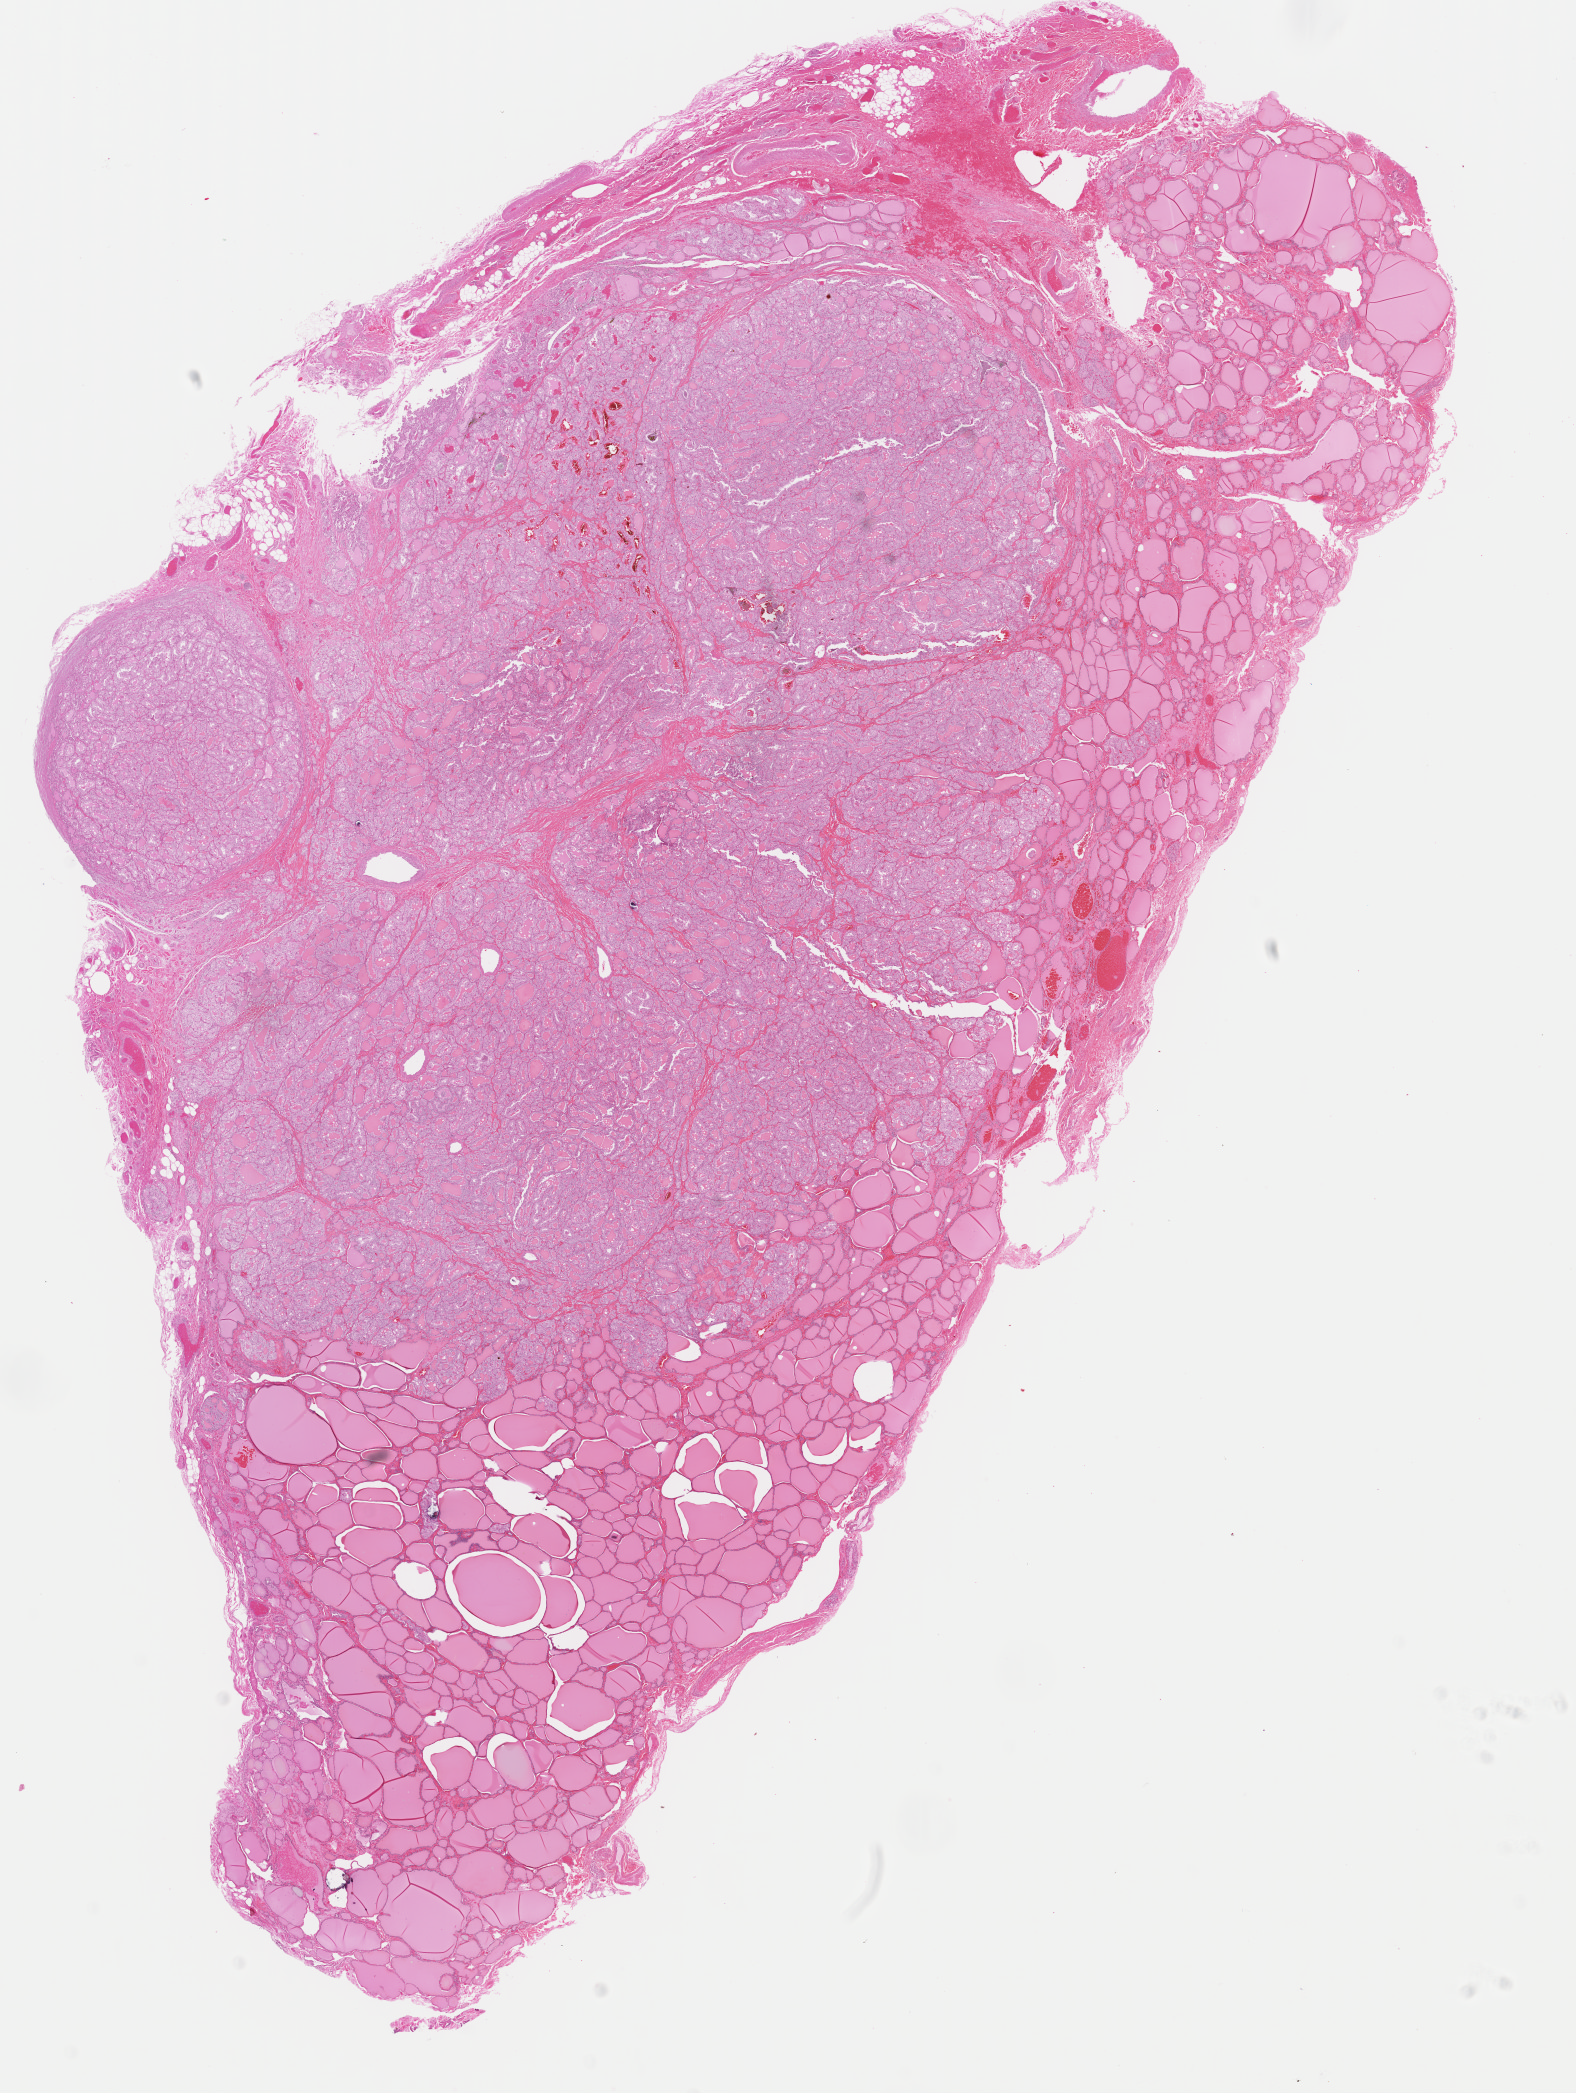
H&E whole-slide image, a low-resolution overview of the entire scanned area, about 12.5 x 16.5 mm (from a 40x scan); FFPE section; primary tumour sample from the thyroid. Female, age 28 years at initial diagnosis.
TNM: T3 N1 M0. Lymph nodes positive (case pathology): 6 of 55 examined. Pathologic diagnosis: Papillary adenocarcinoma, NOS (thyroid gland). Laterality: left. AJCC pathologic stage: I (6th edition).